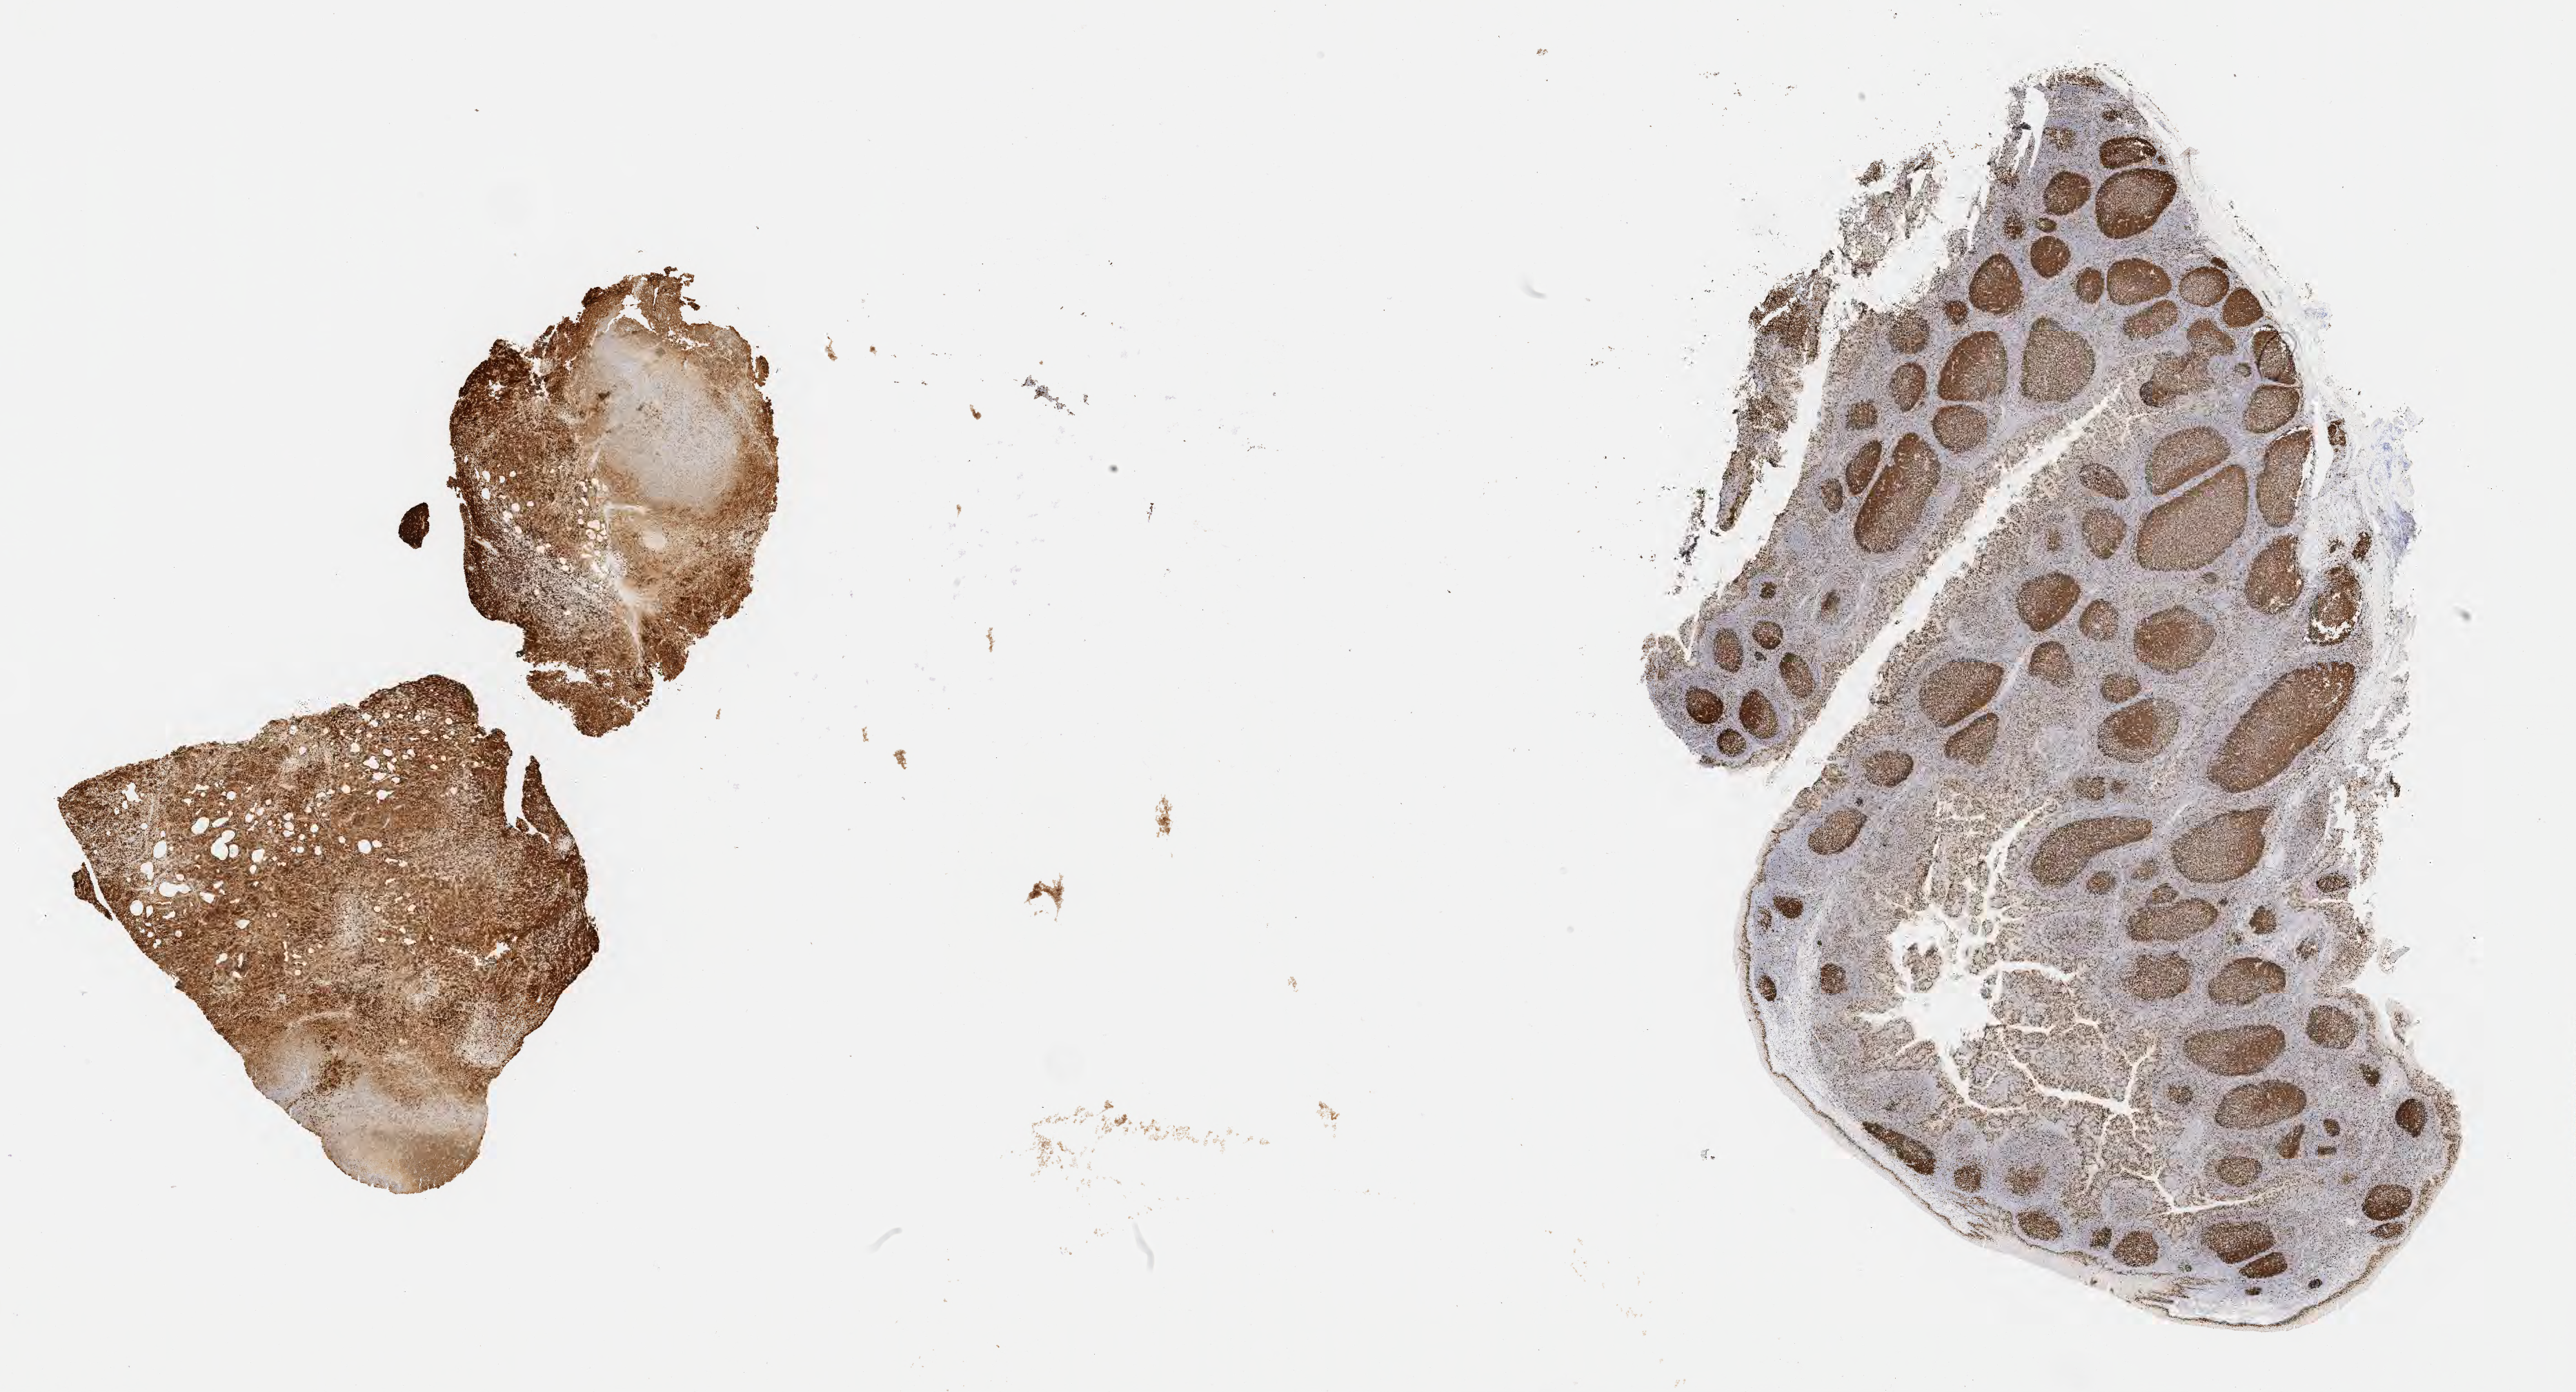
IHC for Ki-67, whole-slide image, low-resolution overview of the scanned area, about 30.2 x 16.3 mm; specimen: tumor tissue; anatomic site: mandible. Male, age 7 years at initial diagnosis.
• histologic diagnosis: Burkitt lymphoma, NOS